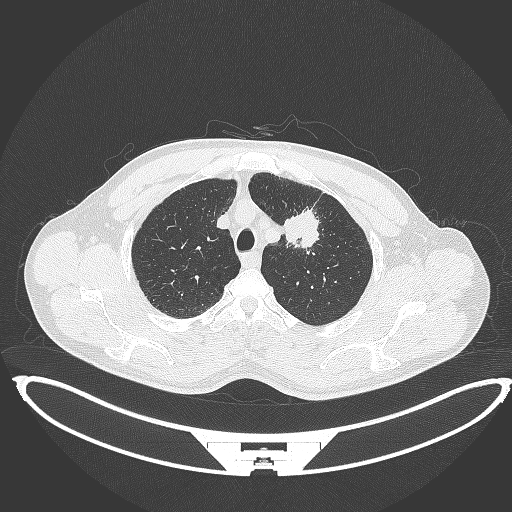
Chest CT, one axial slice. Slice 359 of 395 in the series (ordered by position). Reconstruction kernel B70f. 120 kVp. Lung window (W 1500 / L -600 HU). 1 mm slice thickness. 512 × 512 image matrix. Male patient, age 60 years. Case-level facts recorded for this patient, not image findings: clinical TNM (as recorded): T2a N0 M0; histopathological grade: G1-G2.
Annotated regions visible in this slice (rectangle marked by the reading radiologist):
- lung tumour (recorded histology: squamous cell carcinoma): bounding box [x1, y1, x2, y2] px = [281, 205, 323, 253]